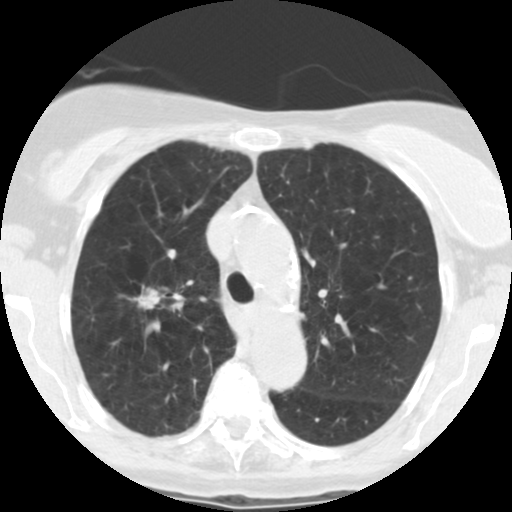
Low-dose screening chest CT, one axial slice; position 180 of 246 along the scan axis; lung window (W 1500 / L -600 HU); 512 × 512 image matrix, field of view 288 × 288 mm.
Outlined on this slice (expert manual segmentation):
- lesion 1 (tumor, upper lobe of right lung): box from (x=129, y=285) to (x=161, y=309) px